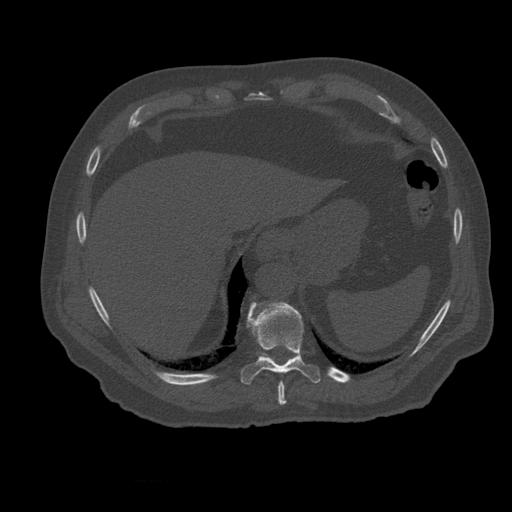
CT including the spine, one axial slice. Slice 302 of 399 in the series (ordered by position). 120 kVp. Bone window (W 1800 / L 400 HU). 1.25 mm slice thickness. 512 × 512 image matrix, field of view 407 × 407 mm. Patient age 73 years. Case-level facts recorded for this patient, not image findings: primary cancer: prostate.
Annotated regions visible in this slice (semi-automatic segmentation, software-assisted and operator-edited):
- T10 vertebra: bounding box <241,303,321,385> (left, top, right, bottom; pixels)
- T11 vertebra: <260,353,276,363>
- T9 vertebra: <278,382,287,405>